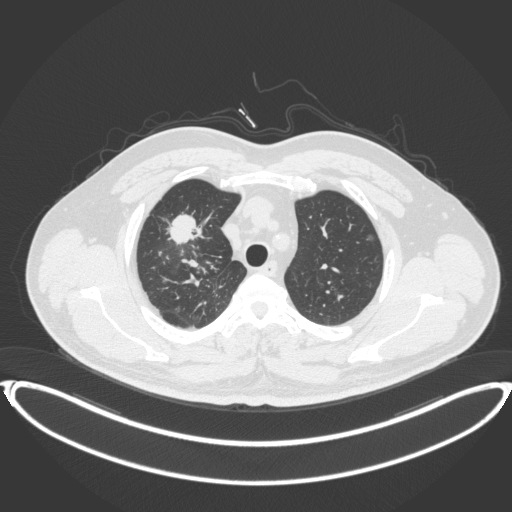
Chest CT, one axial slice. Position 309 of 399 along the scan axis. Lung window (W 1500 / L -600 HU). 1 mm slice thickness. 512 × 512 image matrix, field of view 445 × 445 mm. Patient: male, 53 years. From the clinical record (not read from this slice): clinical TNM (as recorded): T2a N0 M0.
Annotated regions visible in this slice (bounding box drawn by a radiologist):
- lung tumour (recorded histology: adenocarcinoma): bounding box <168,211,208,248> (left, top, right, bottom; pixels)